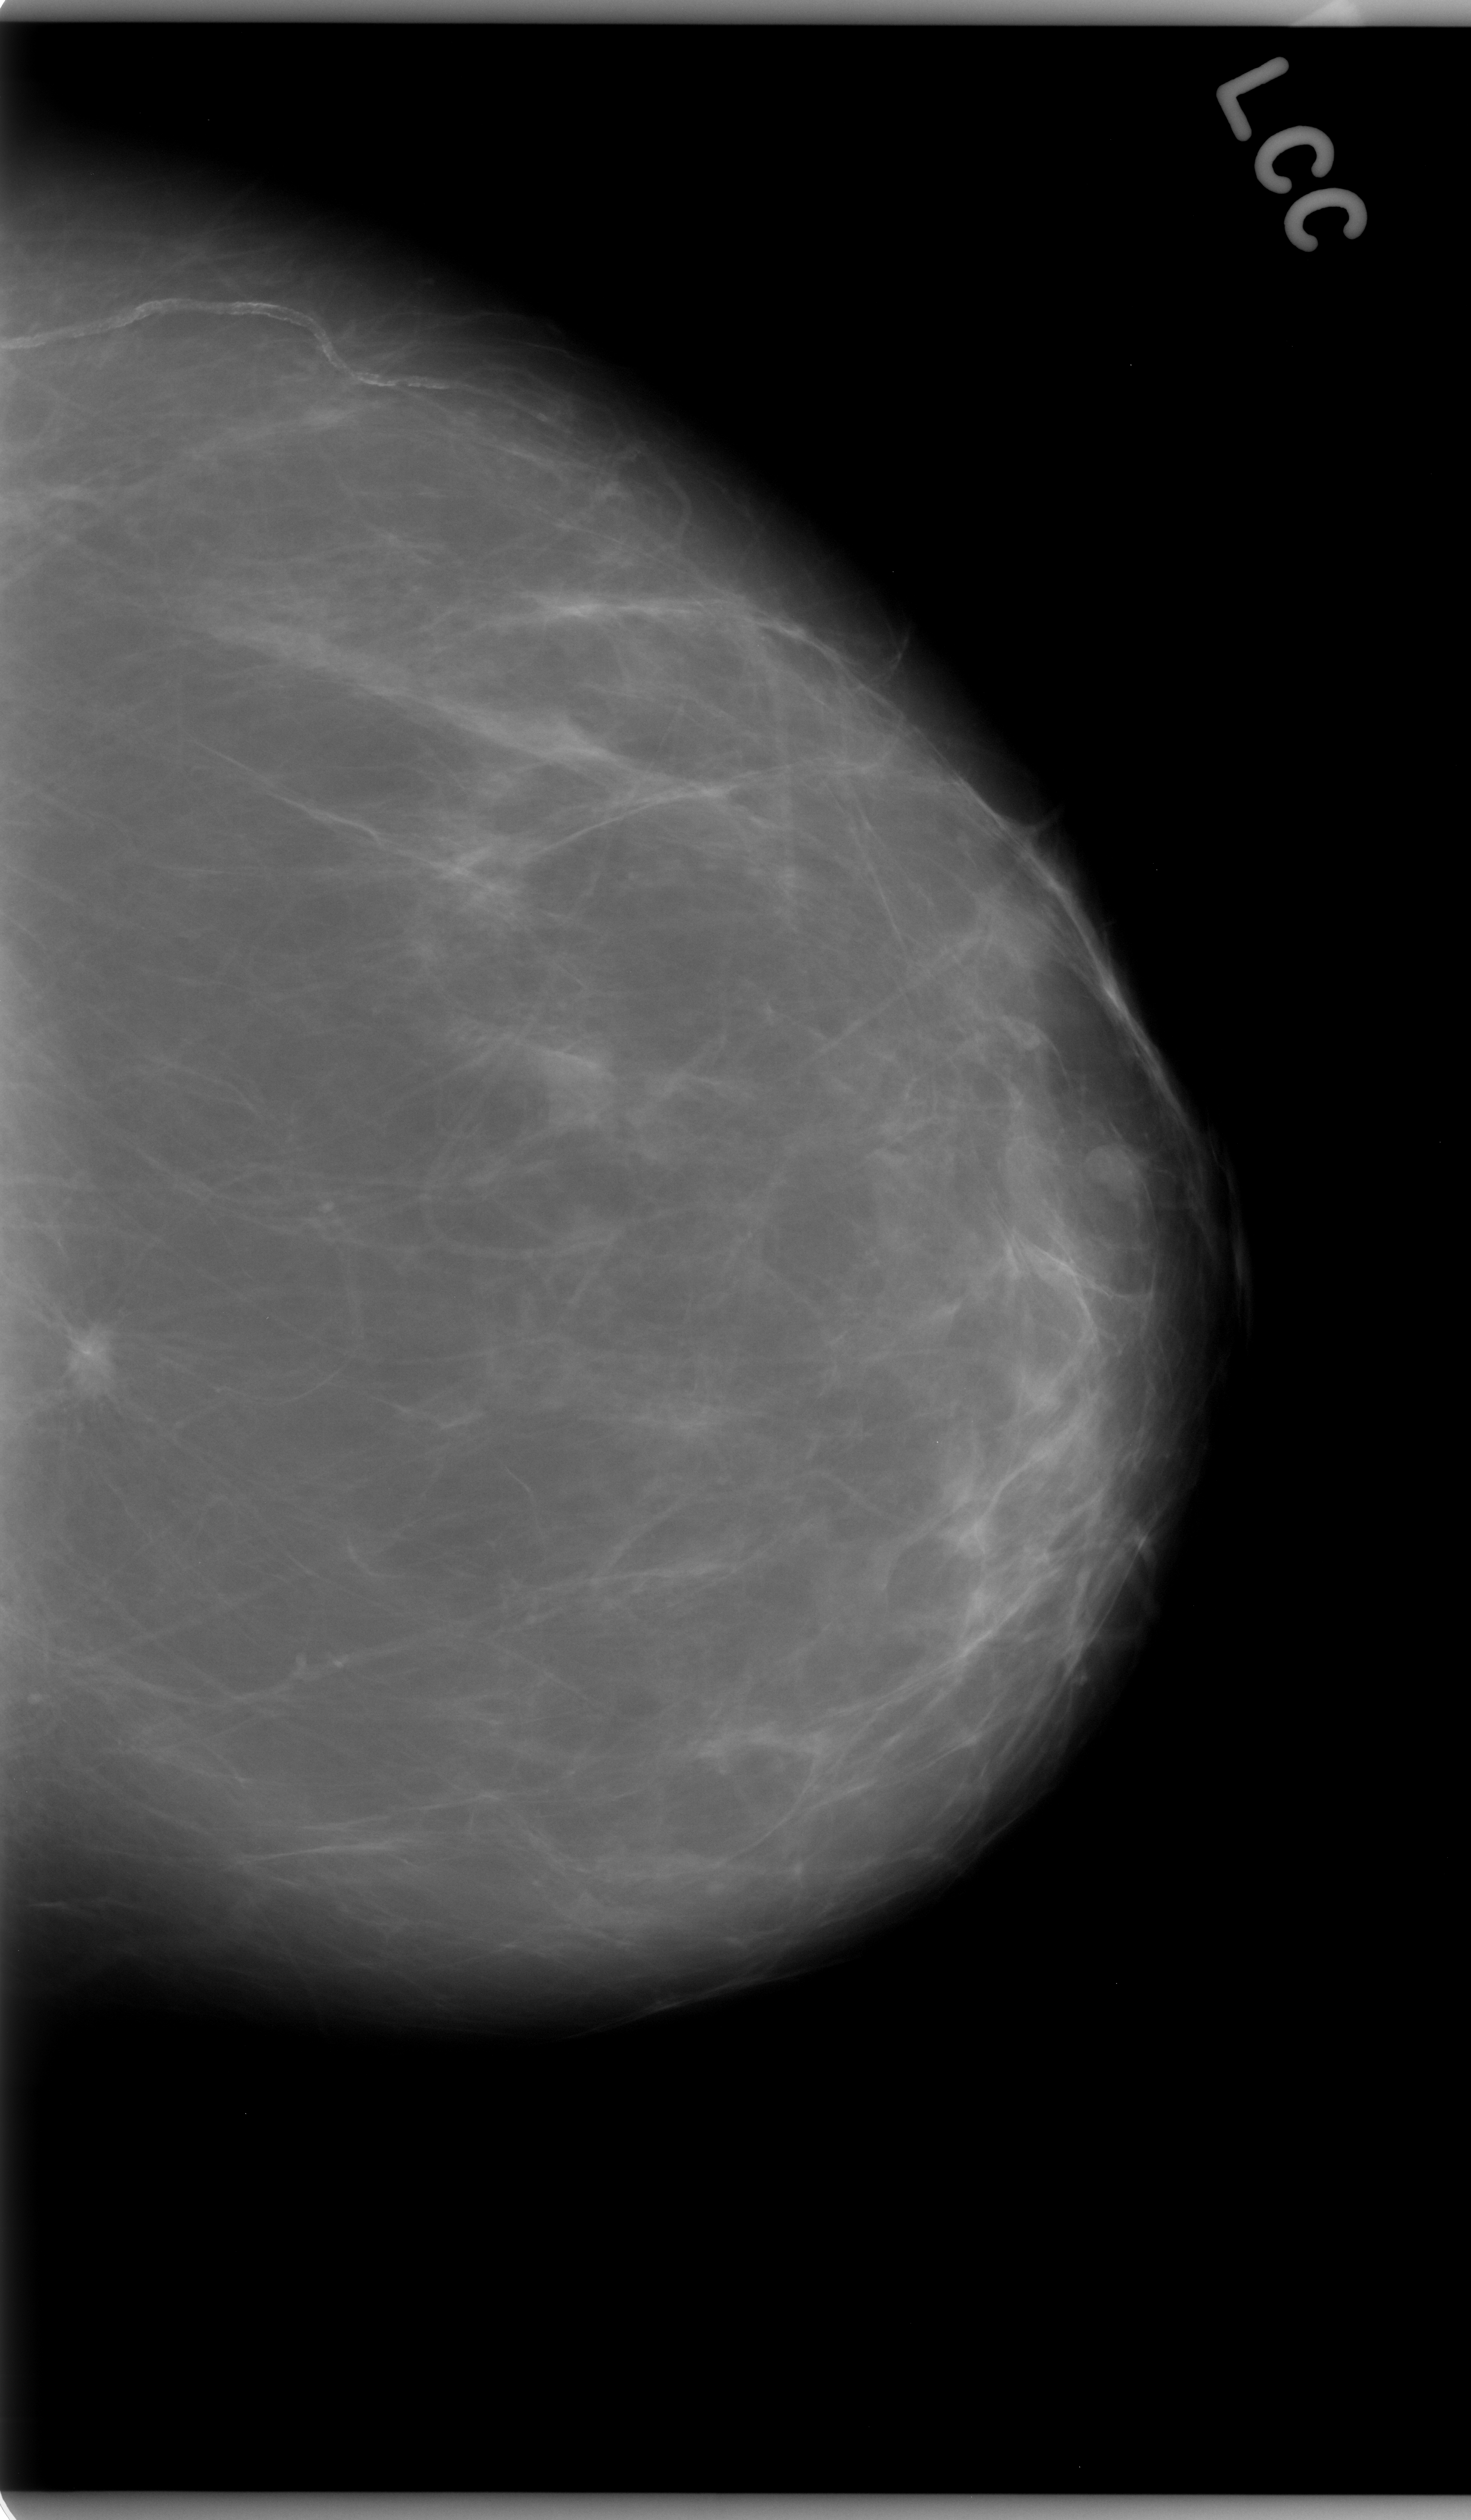
Scanned film-screen mammogram. Left breast. Craniocaudal (CC) view. Breast composition: almost entirely fatty (BI-RADS density category 1 of 4). 1471 × 2520 image matrix.
Marked abnormalities (boxes around the expert regions of interest):
- mass, shape irregular, margins spiculated; BI-RADS assessment category 5; pathology result (as recorded, not read from the image): malignant: box from (x=27, y=1297) to (x=127, y=1407) px